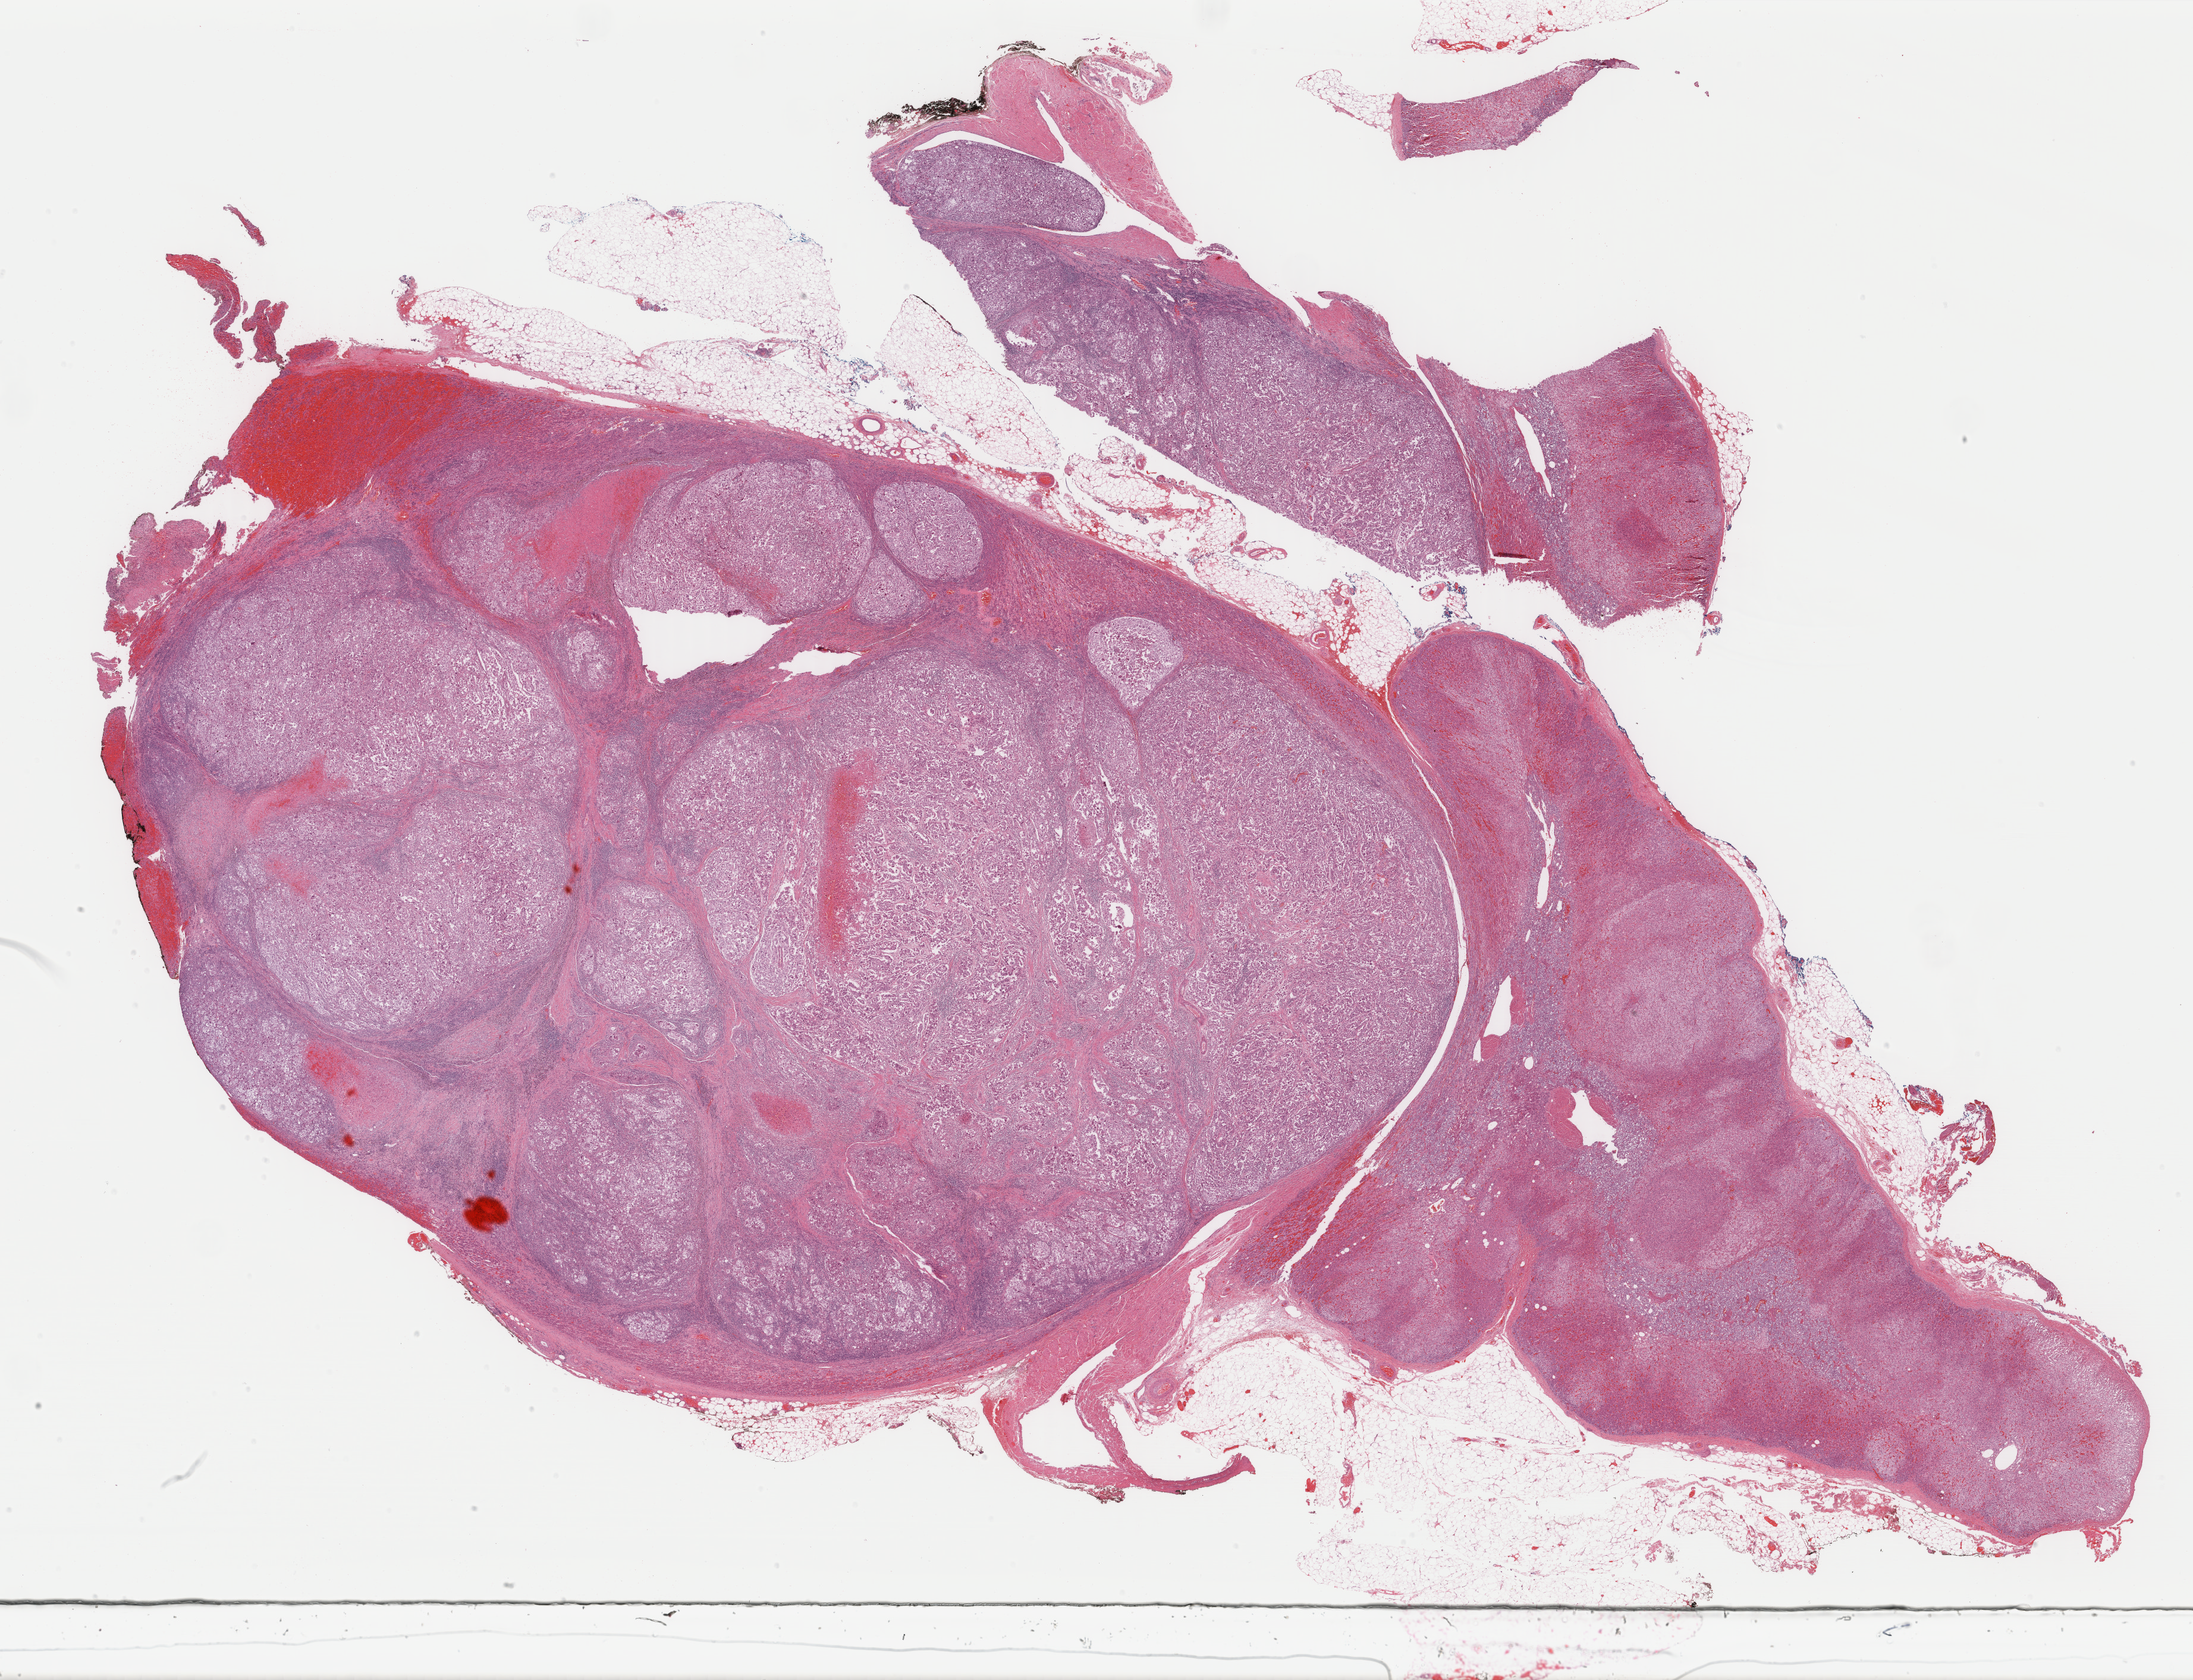
Hematoxylin and eosin (H&E) stained whole-slide image, shown as a low-resolution overview of the whole scanned area (about 29.3 x 22.4 mm), formalin-fixed paraffin-embedded (FFPE) diagnostic section, metastatic tumour sample, sampled site: adrenal gland. Male patient; age at initial diagnosis 49 years.
This section: metastatic tumour tissue. Patient diagnosis: Malignant melanoma, NOS.